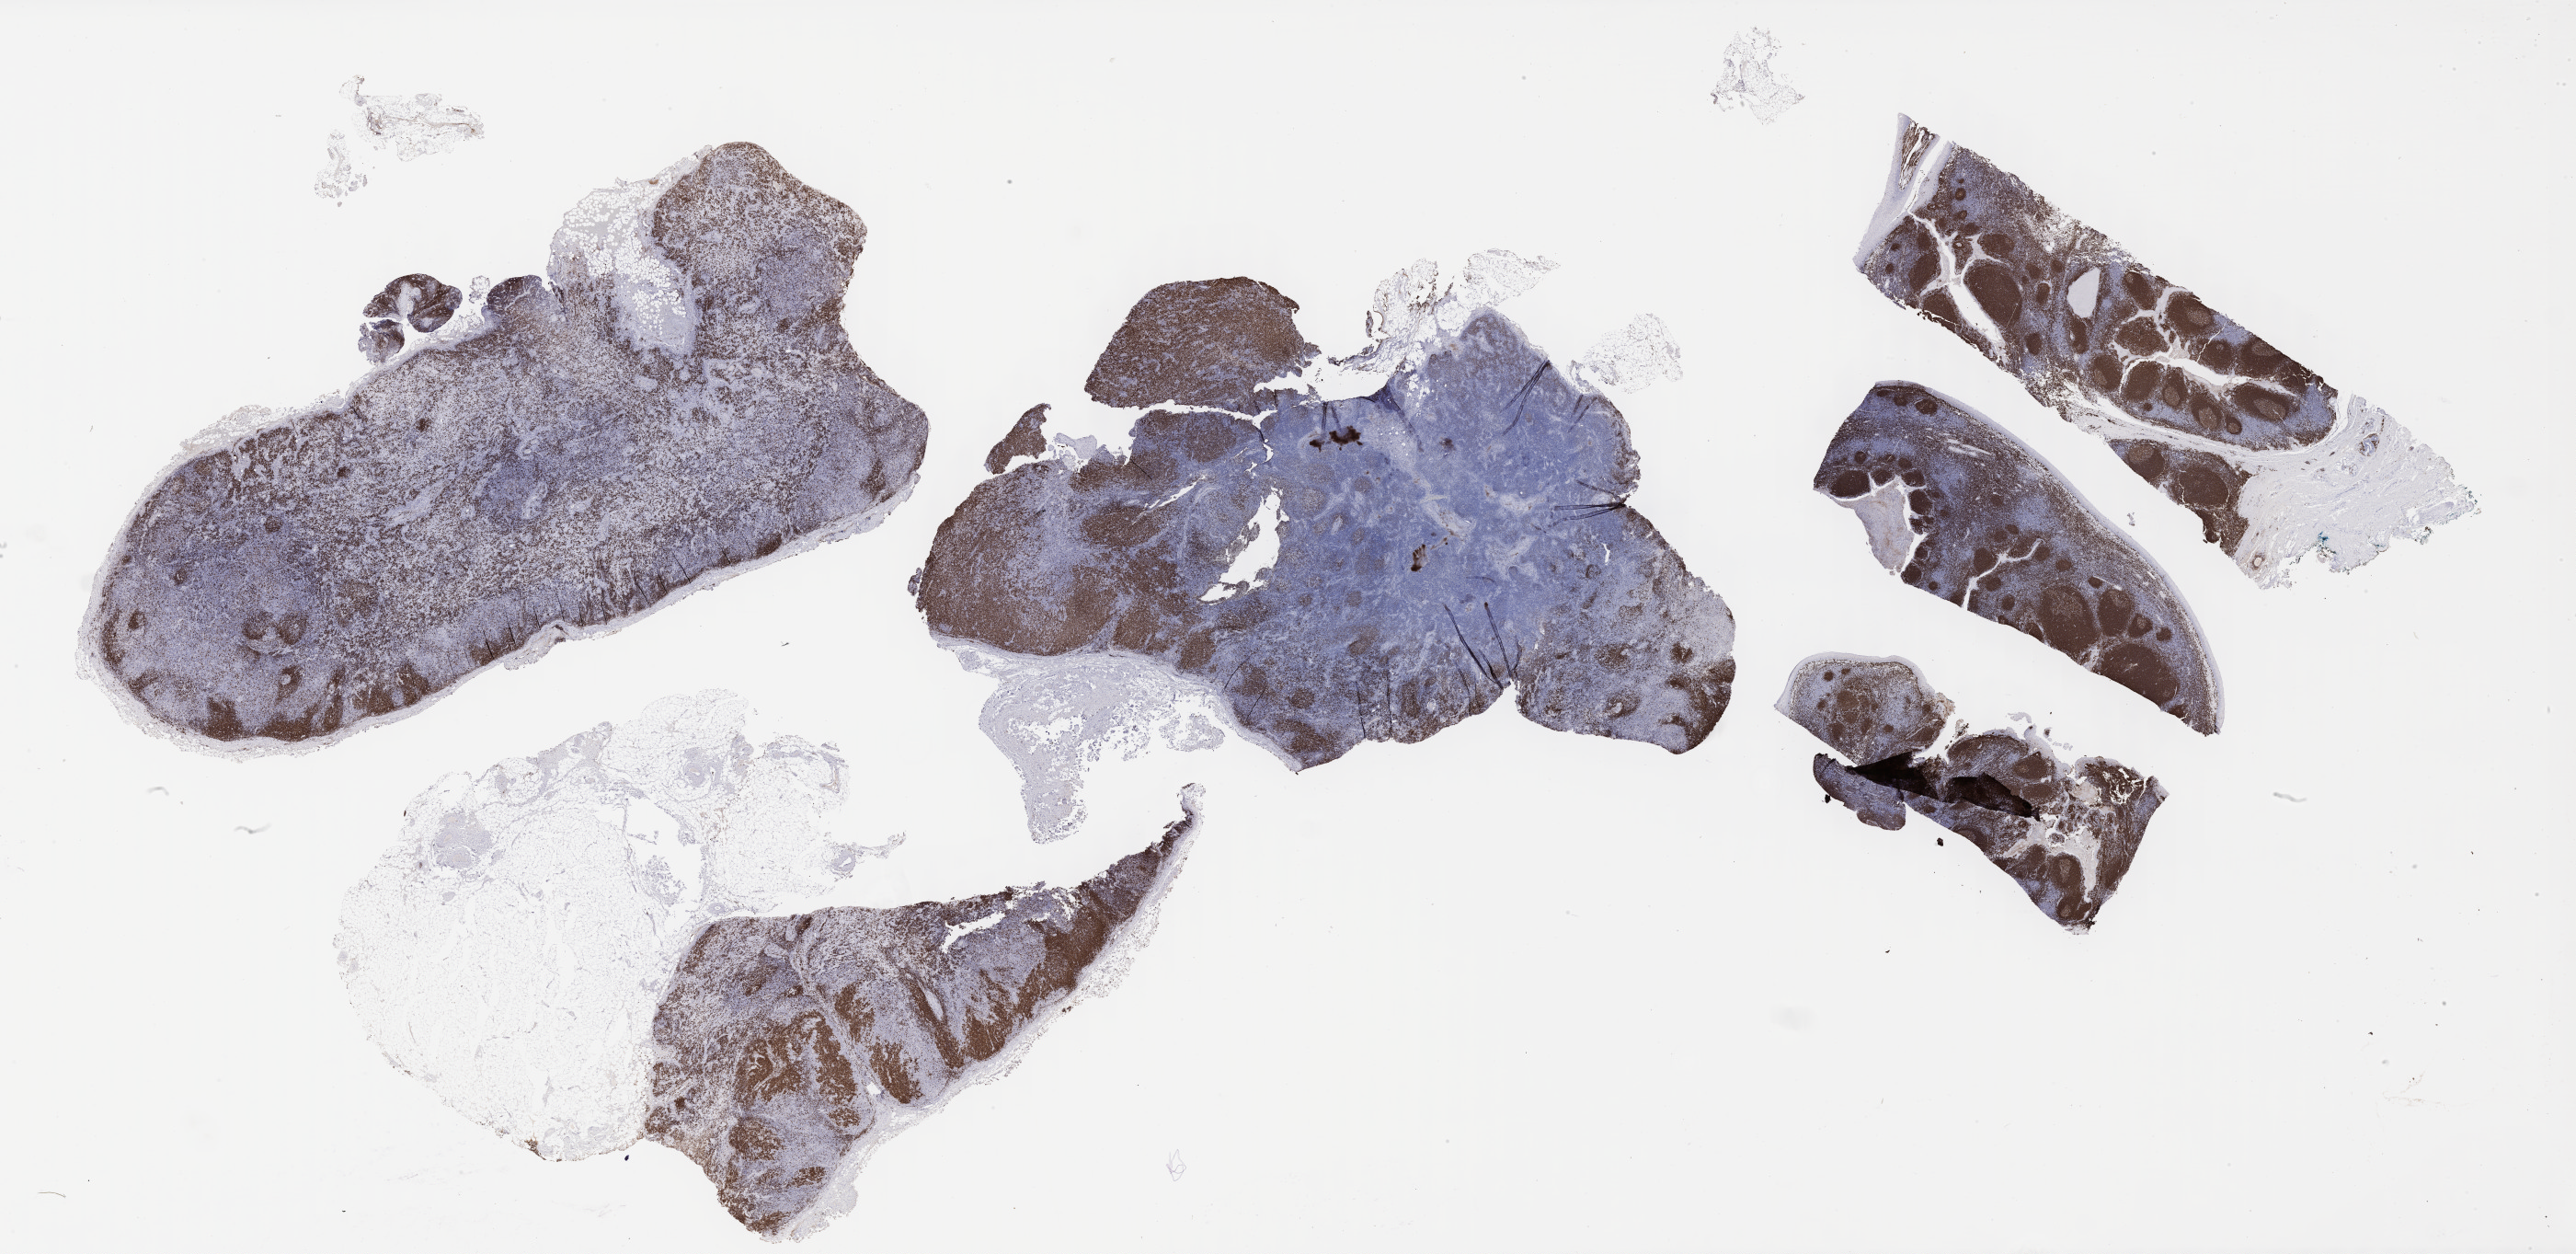
IHC for CD79a, whole-slide image, shown as a low-resolution overview of the whole scanned area (about 45.3 x 22.0 mm), tumor tissue, site: lymph node. Patient: male, 56 years old.
* diagnosis: Diffuse large B-cell lymphoma, NOS